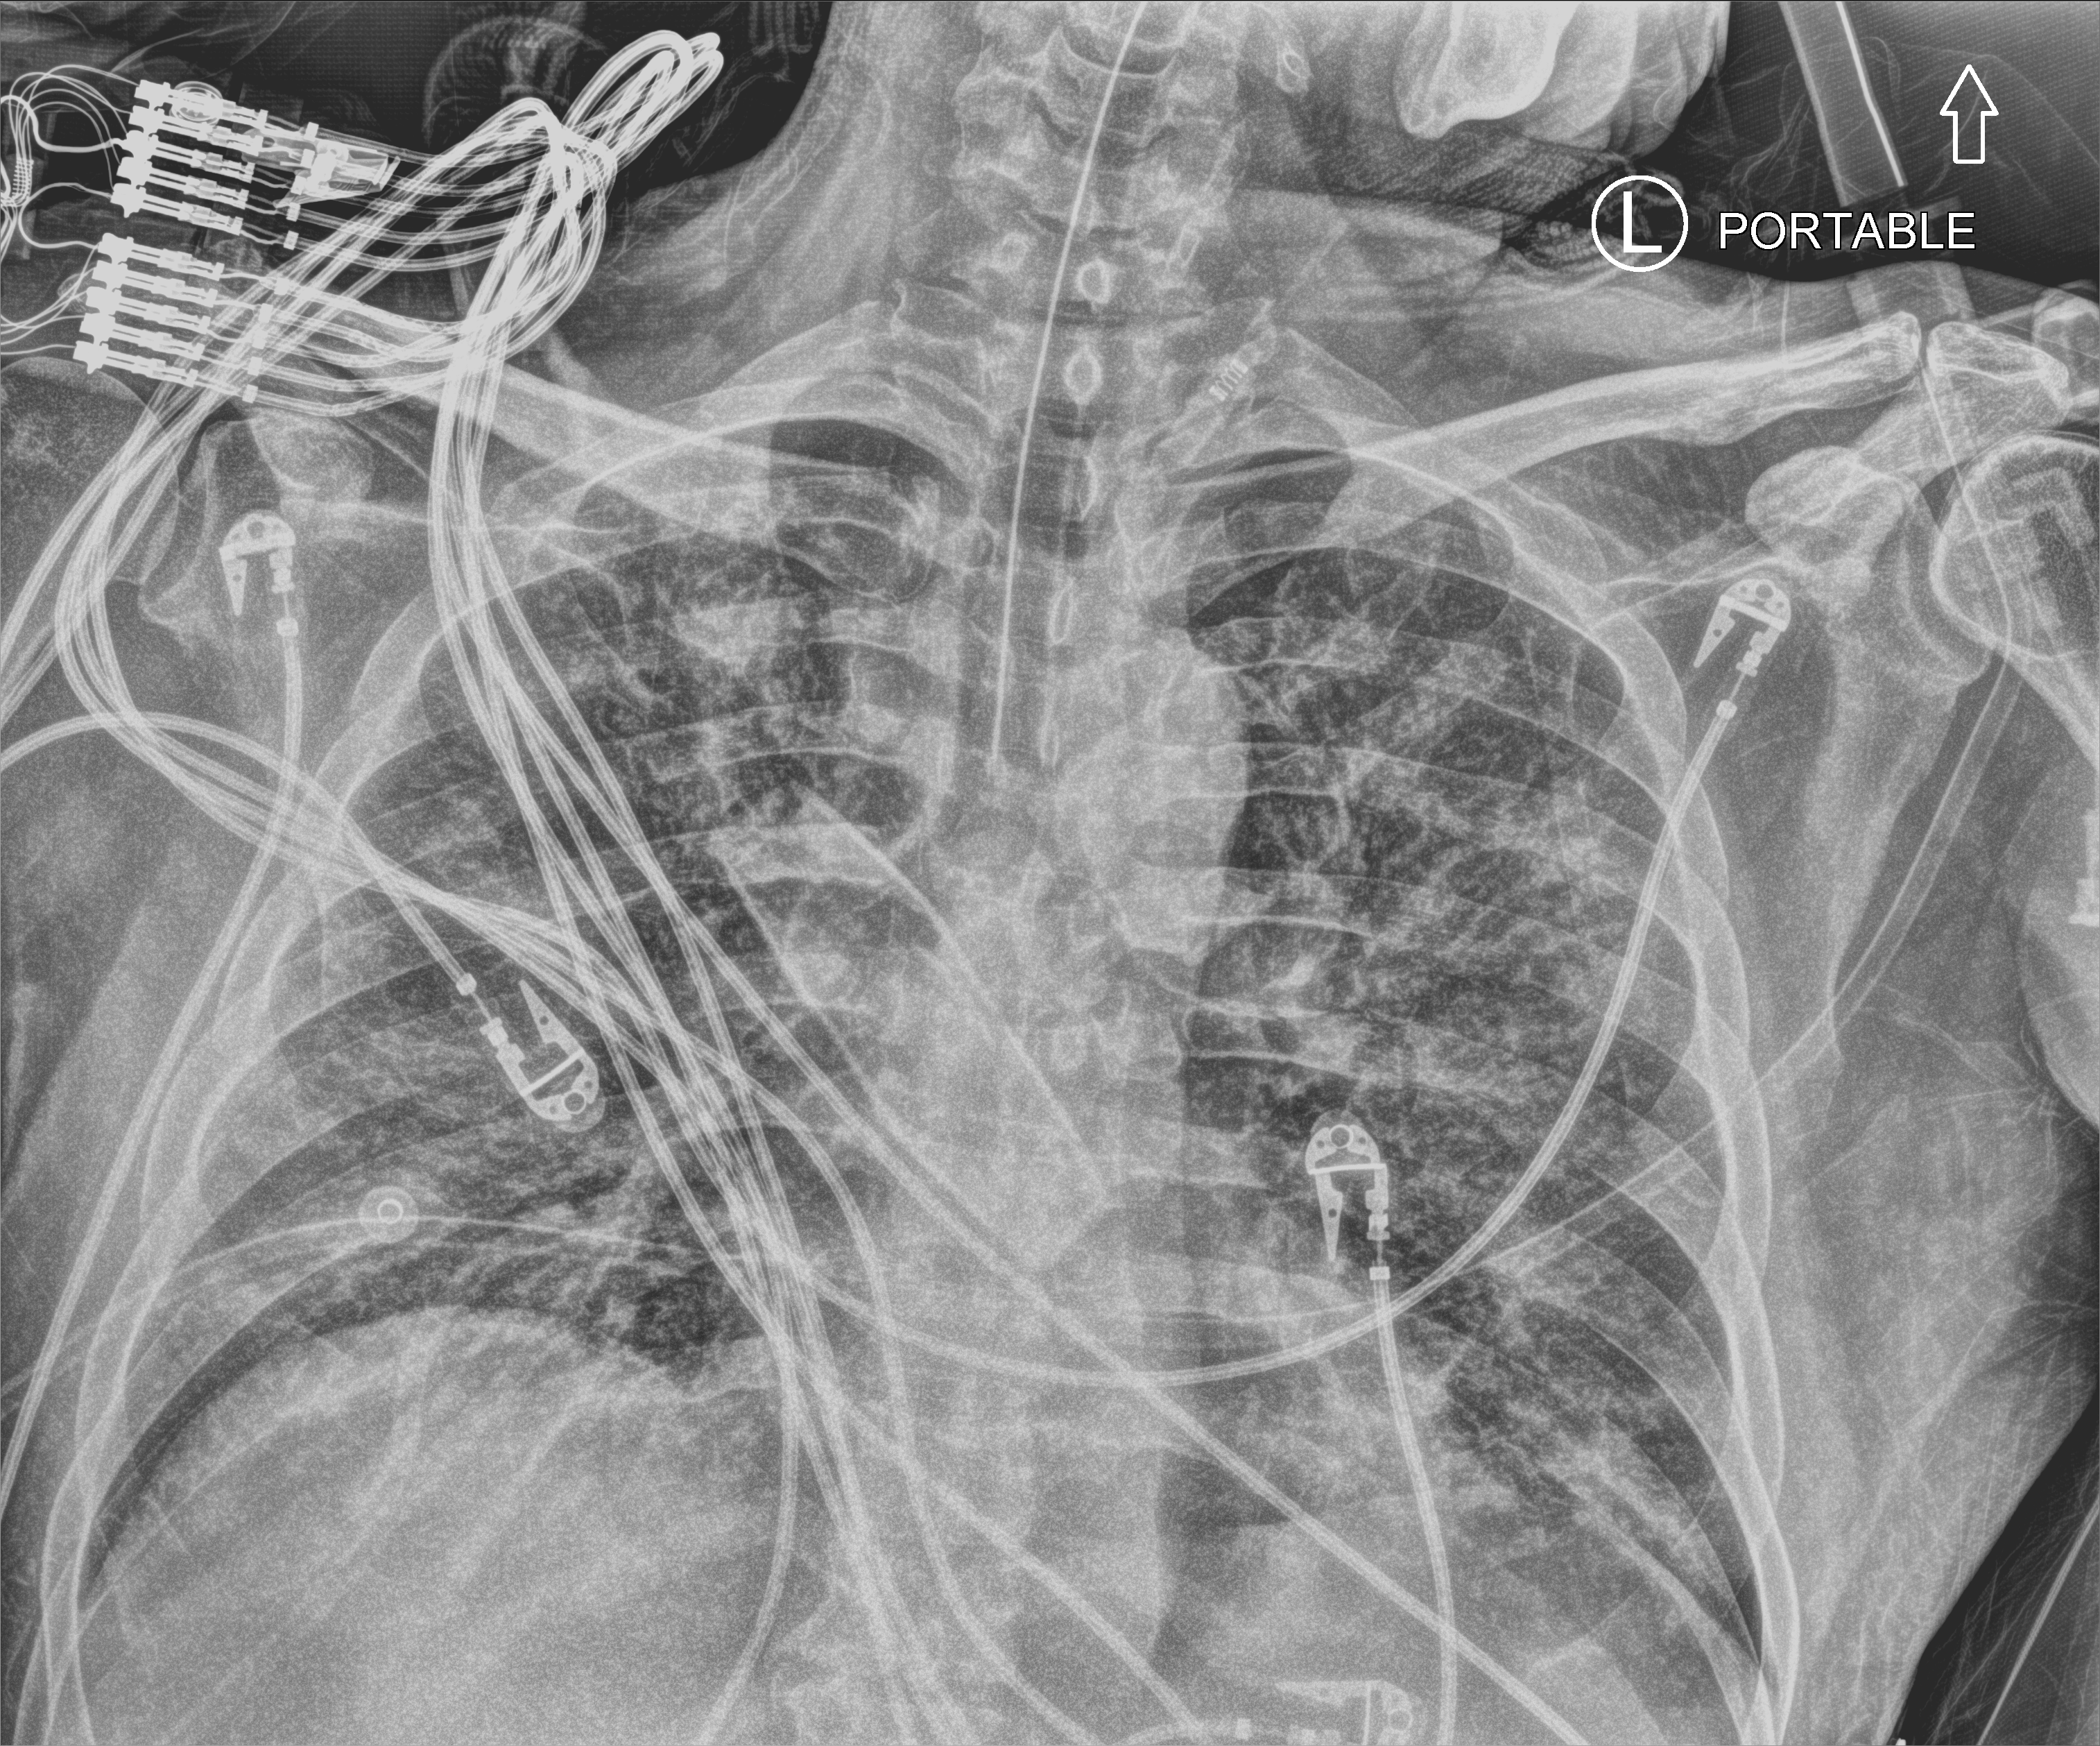
Portable chest radiograph. Male patient hospitalised with COVID-19, age 18–59 years.
From the hospital-stay record, not from the radiograph (when in the stay this image was taken is not recorded):
- mechanically ventilated during this hospital stay: yes
- COPD (admission record): no
- length of hospital stay: 40 days